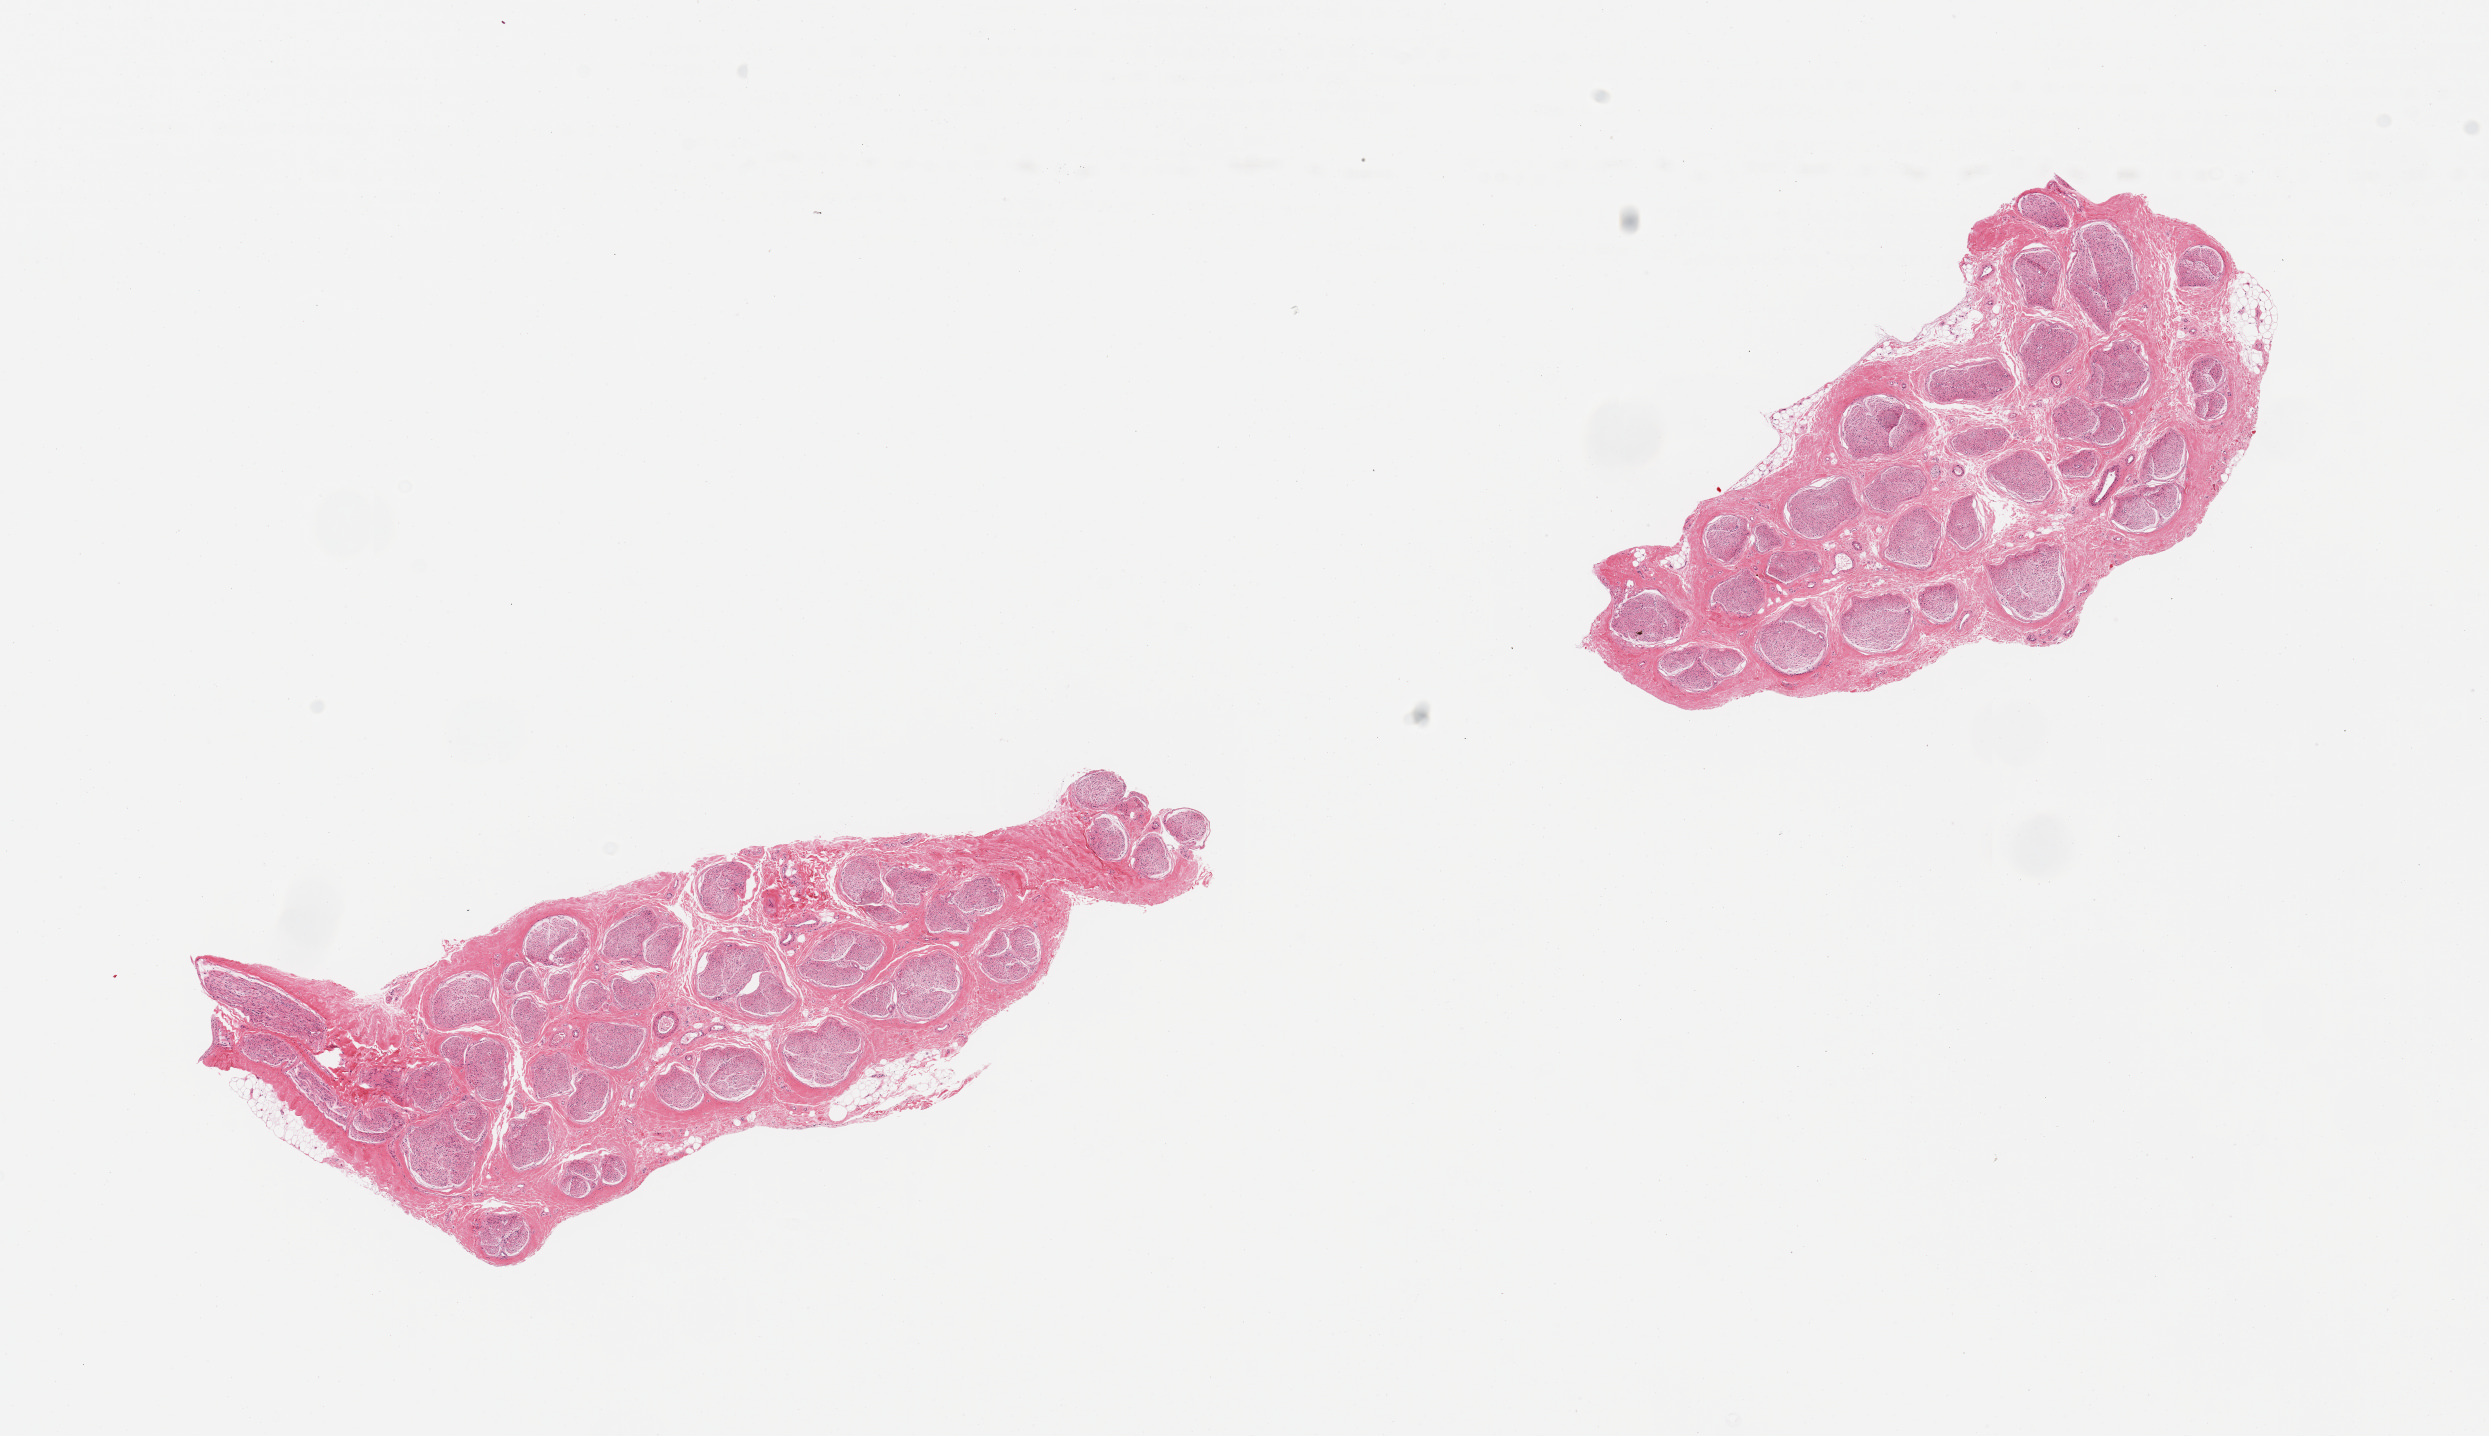
Haematoxylin and eosin whole-slide image — low-resolution overview of the scanned area, about 19.7 x 11.4 mm (acquisition: 20x scan), PAXgene-fixed, paraffin-embedded tissue, target tissue: tibial nerve, tissue donor sample. Donor: male.
- review note (as recorded): 2 pieces, excellent clean specimens